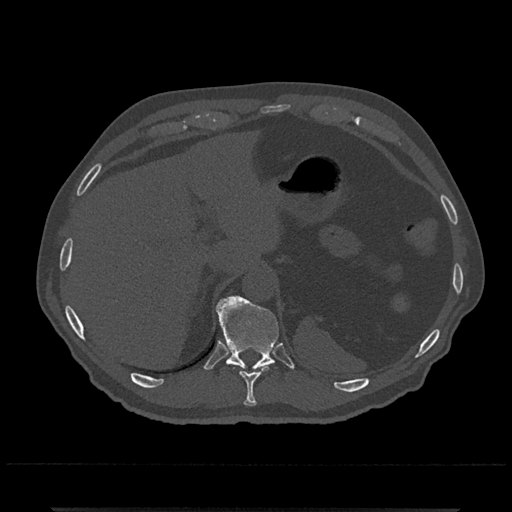
CT including the spine, one axial slice. Position 520 of 797 along the scan axis. Reconstruction kernel Br40s/3. 120 kVp. Bone window (W 1800 / L 400 HU). 0.5 mm slice thickness. 512 × 512 image matrix. Male patient, age 67 years. Case-level facts recorded for this patient, not image findings: primary cancer: prostate.
Outlined on this slice (semi-automatically segmented with operator editing):
- T10 vertebra: bounding box <240,367,267,407> (left, top, right, bottom; pixels)
- T11 vertebra: <216,296,279,369>